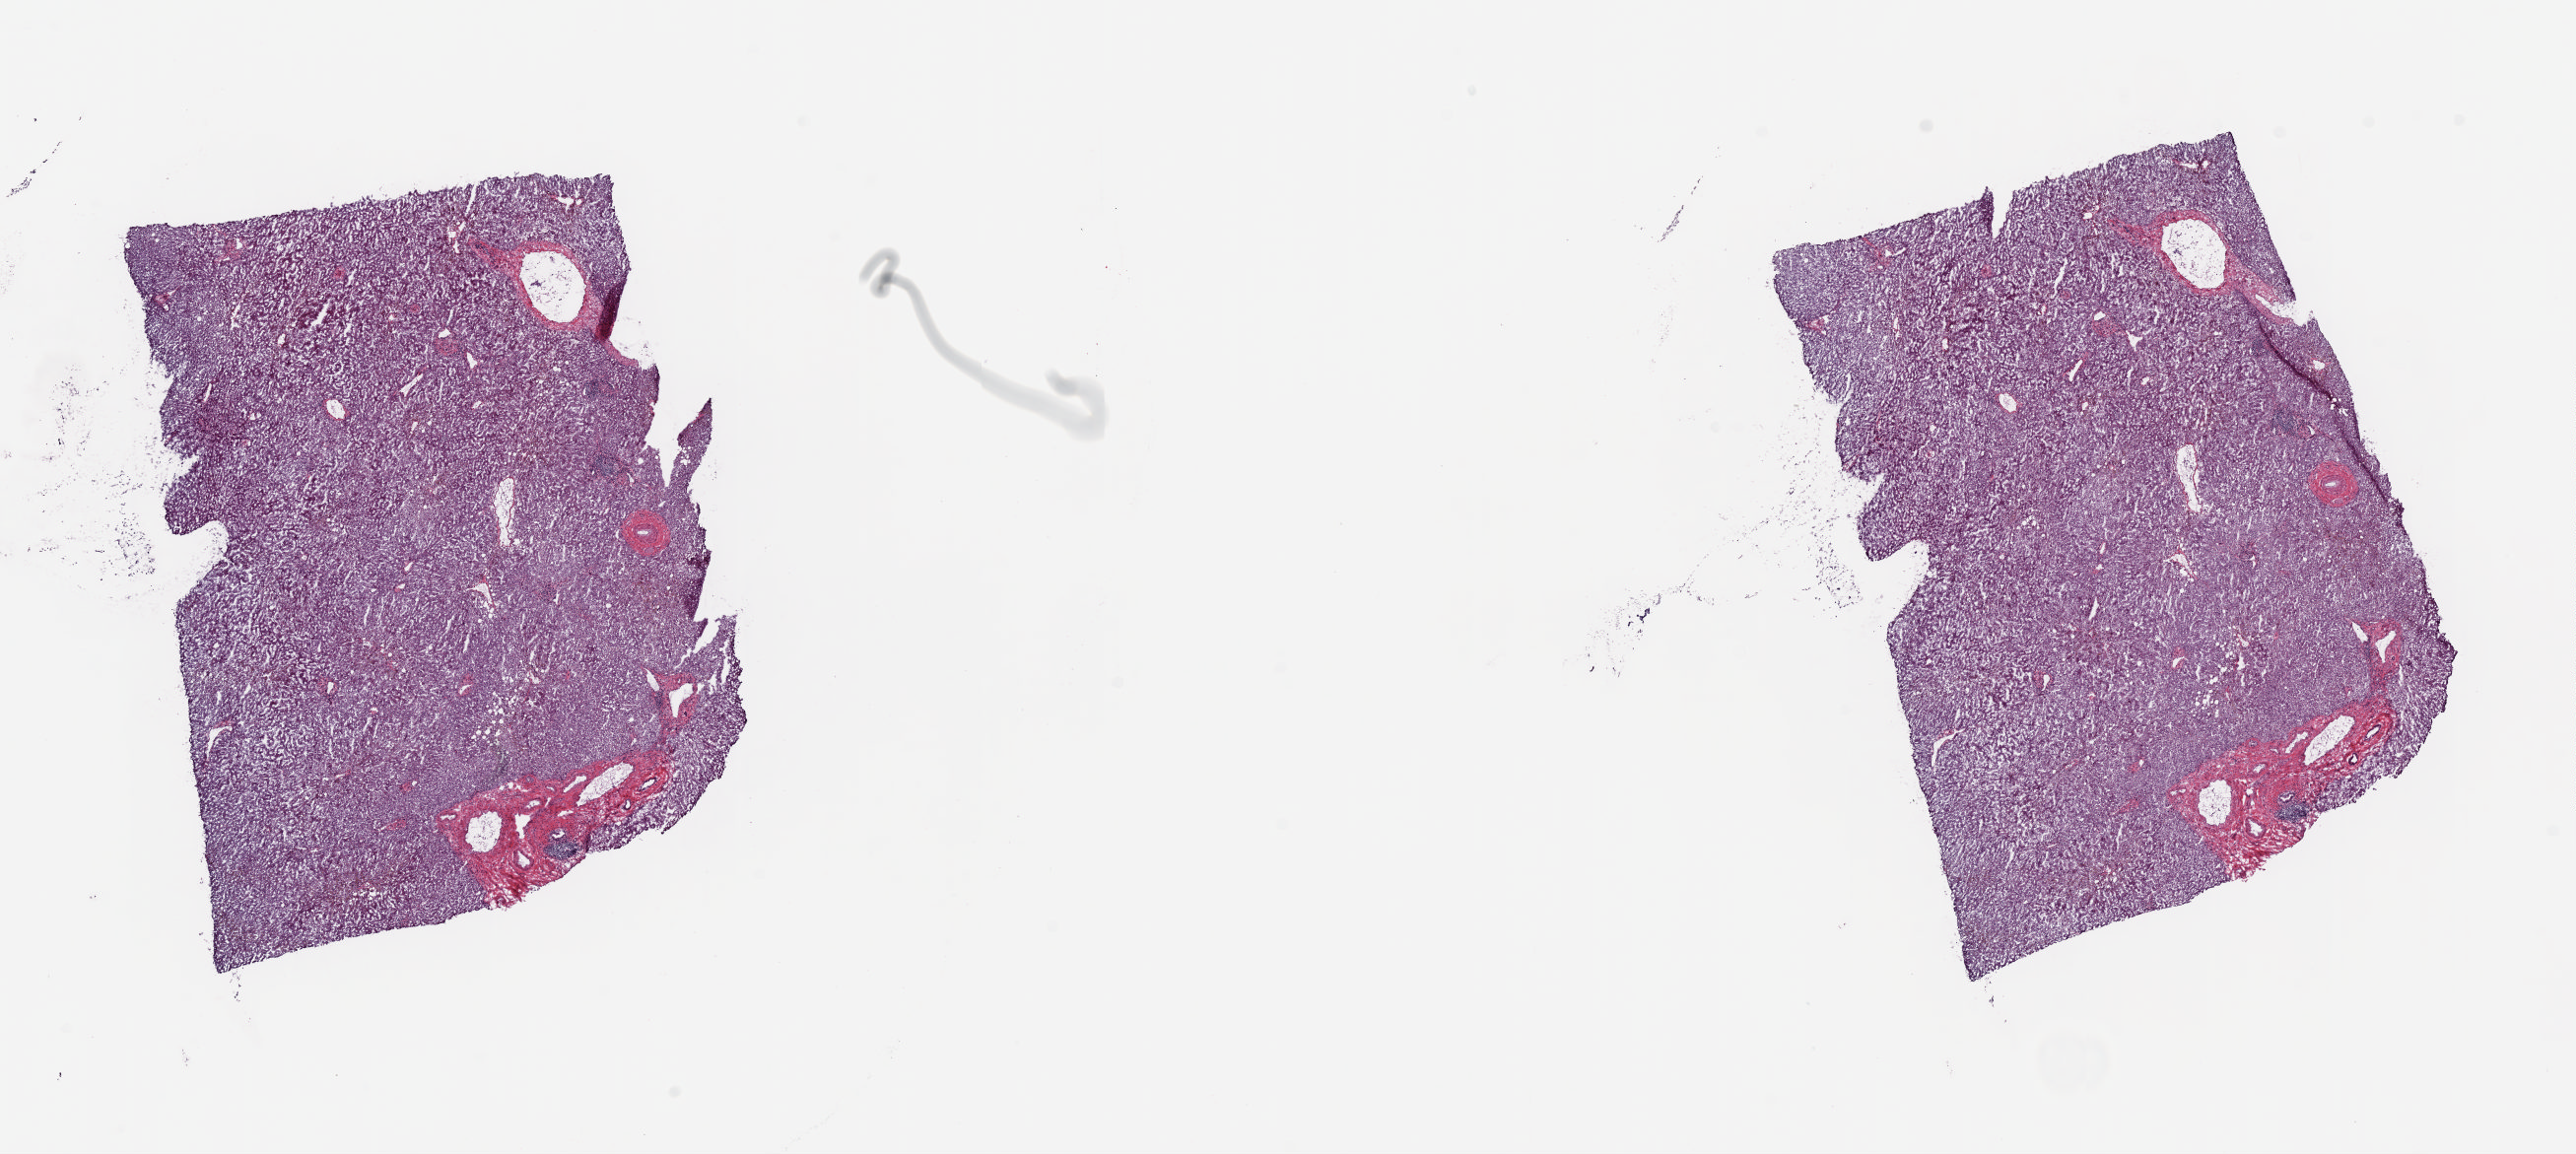
Digitized H&E-stained tissue section (whole slide) — a low-resolution overview of the entire scanned area, about 20.7 x 9.3 mm (from a 20x scan); frozen section from the top of the tissue portion; solid tissue normal (non-tumour tissue) sample from the liver. Patient: female, age at initial diagnosis 81 years. Slide review estimates, as recorded: tumour cells 0%, tumour nuclei 0%, normal cells 90%, stromal cells 10%, necrosis 0%. Inflammatory infiltration, as recorded: lymphocyte infiltration 1%, monocyte infiltration 1%, neutrophil infiltration 1%.
• this section: solid tissue normal (non-tumour) sample from the same patient
• patient diagnosis: Hepatocellular carcinoma, NOS